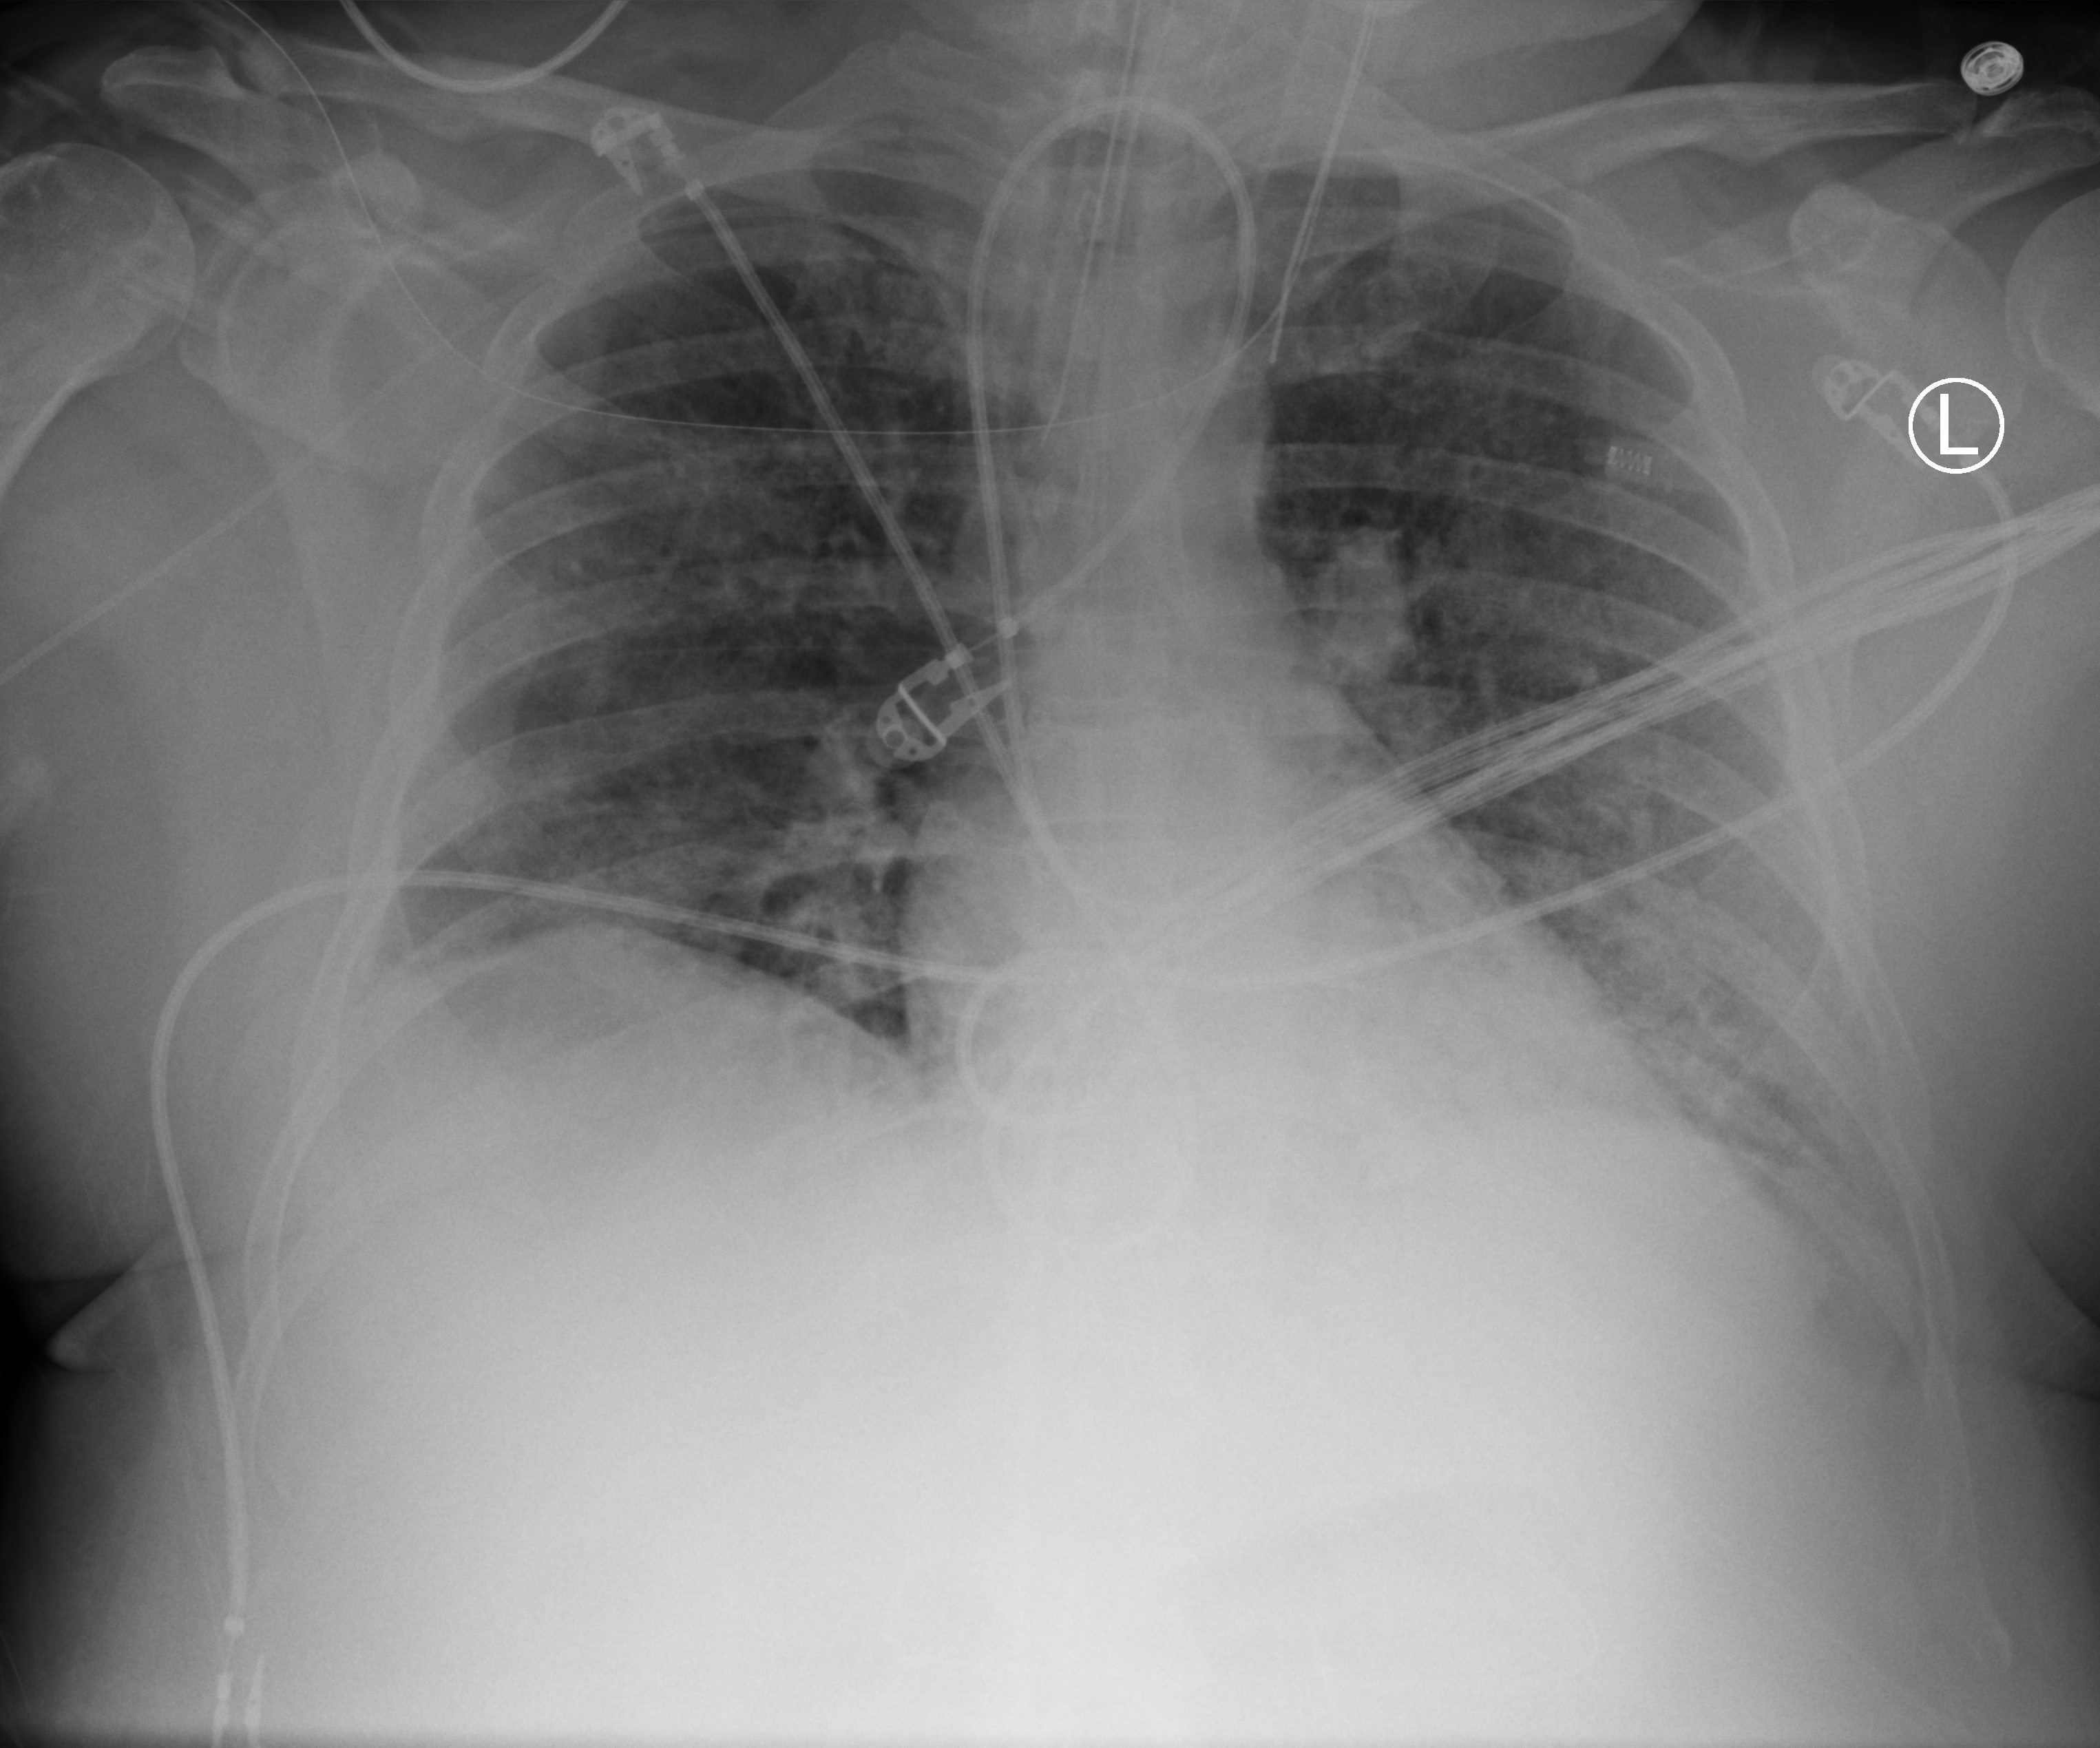
Bedside chest radiograph (computed radiography). Patient hospitalised with COVID-19; male, aged 18–59 years.
Admission-level facts for this patient (not findings on this image; timing relative to this image not recorded): COPD (admission record): no; length of hospital stay: 96 days; admitted to intensive care during this hospital stay: yes.